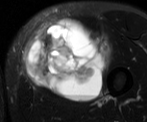
MRI of an extremity soft-tissue mass, one axial slice. Slice 26 of 52 in the series (ordered by position). T2-weighted fat-saturated. MR volume resampled by the dataset authors to the PET/CT grid (not the native acquisition matrix). 3.27 mm slice thickness. 147 × 122 image matrix. Male patient. Case-level facts recorded for this patient, not image findings: histological type: pleiomorphic liposarcoma; grade: high; site of the primary tumour: left thigh.
Structures marked on this image (expert contour drawn on MRI and transferred to this co-registered scan by the dataset authors):
- gross tumour volume including surrounding oedema: bounding box <21,18,113,102> (left, top, right, bottom; pixels)
- gross tumour volume (mass): <21,18,108,102>